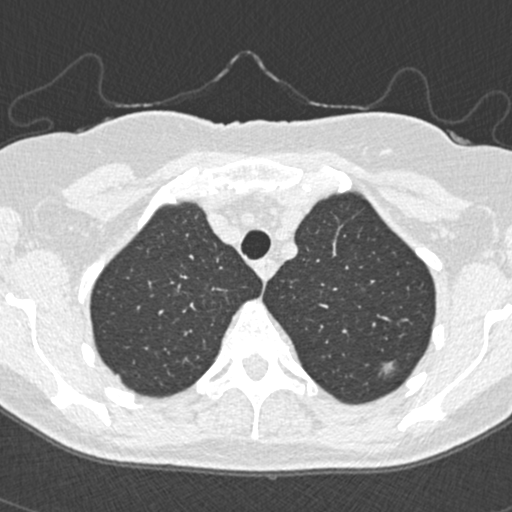
Low-dose screening chest CT, one axial slice; slice 300 of 350 in the series (ordered by position); reconstruction kernel B30f; lung window (W 1500 / L -600 HU); 1 mm slice thickness; 512 × 512 image matrix, field of view 298 × 298 mm.
Annotated regions visible in this slice (manually delineated by an expert):
- lesion 2 (tumor, upper lobe of left lung): bounding box <381,362,395,374> (left, top, right, bottom; pixels)